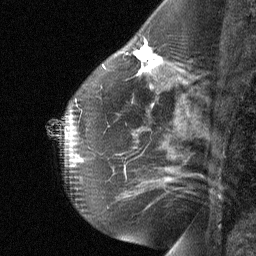
Breast MRI (dynamic contrast-enhanced), one sagittal slice. Position 40 of 64 along the scan axis. Dynamic contrast-enhanced study with each time point stored as its own series, time point 2 of 3 at this slice position (early post-contrast, ordered by acquisition time). 1.5 T. TE 4.8 ms, TR 27 ms. 2 mm slice thickness. 256 × 256 image matrix, field of view 180 × 180 mm. Female patient, age 51 years. From the clinical record (not read from this slice): setting: breast cancer imaged before/during neoadjuvant chemotherapy; receptor status: HR-positive, HER2-negative.
Structures marked on this image (semi-automatically segmented with operator editing):
- analysis volume of interest (the breast-tissue region the enhancement analysis was run in; not a lesion): box from (x=81, y=35) to (x=179, y=103) px
- tumour enhancement mask (voxels above the 90 % enhancement threshold inside the analysis volume of interest): (x=134, y=46)–(x=161, y=70)